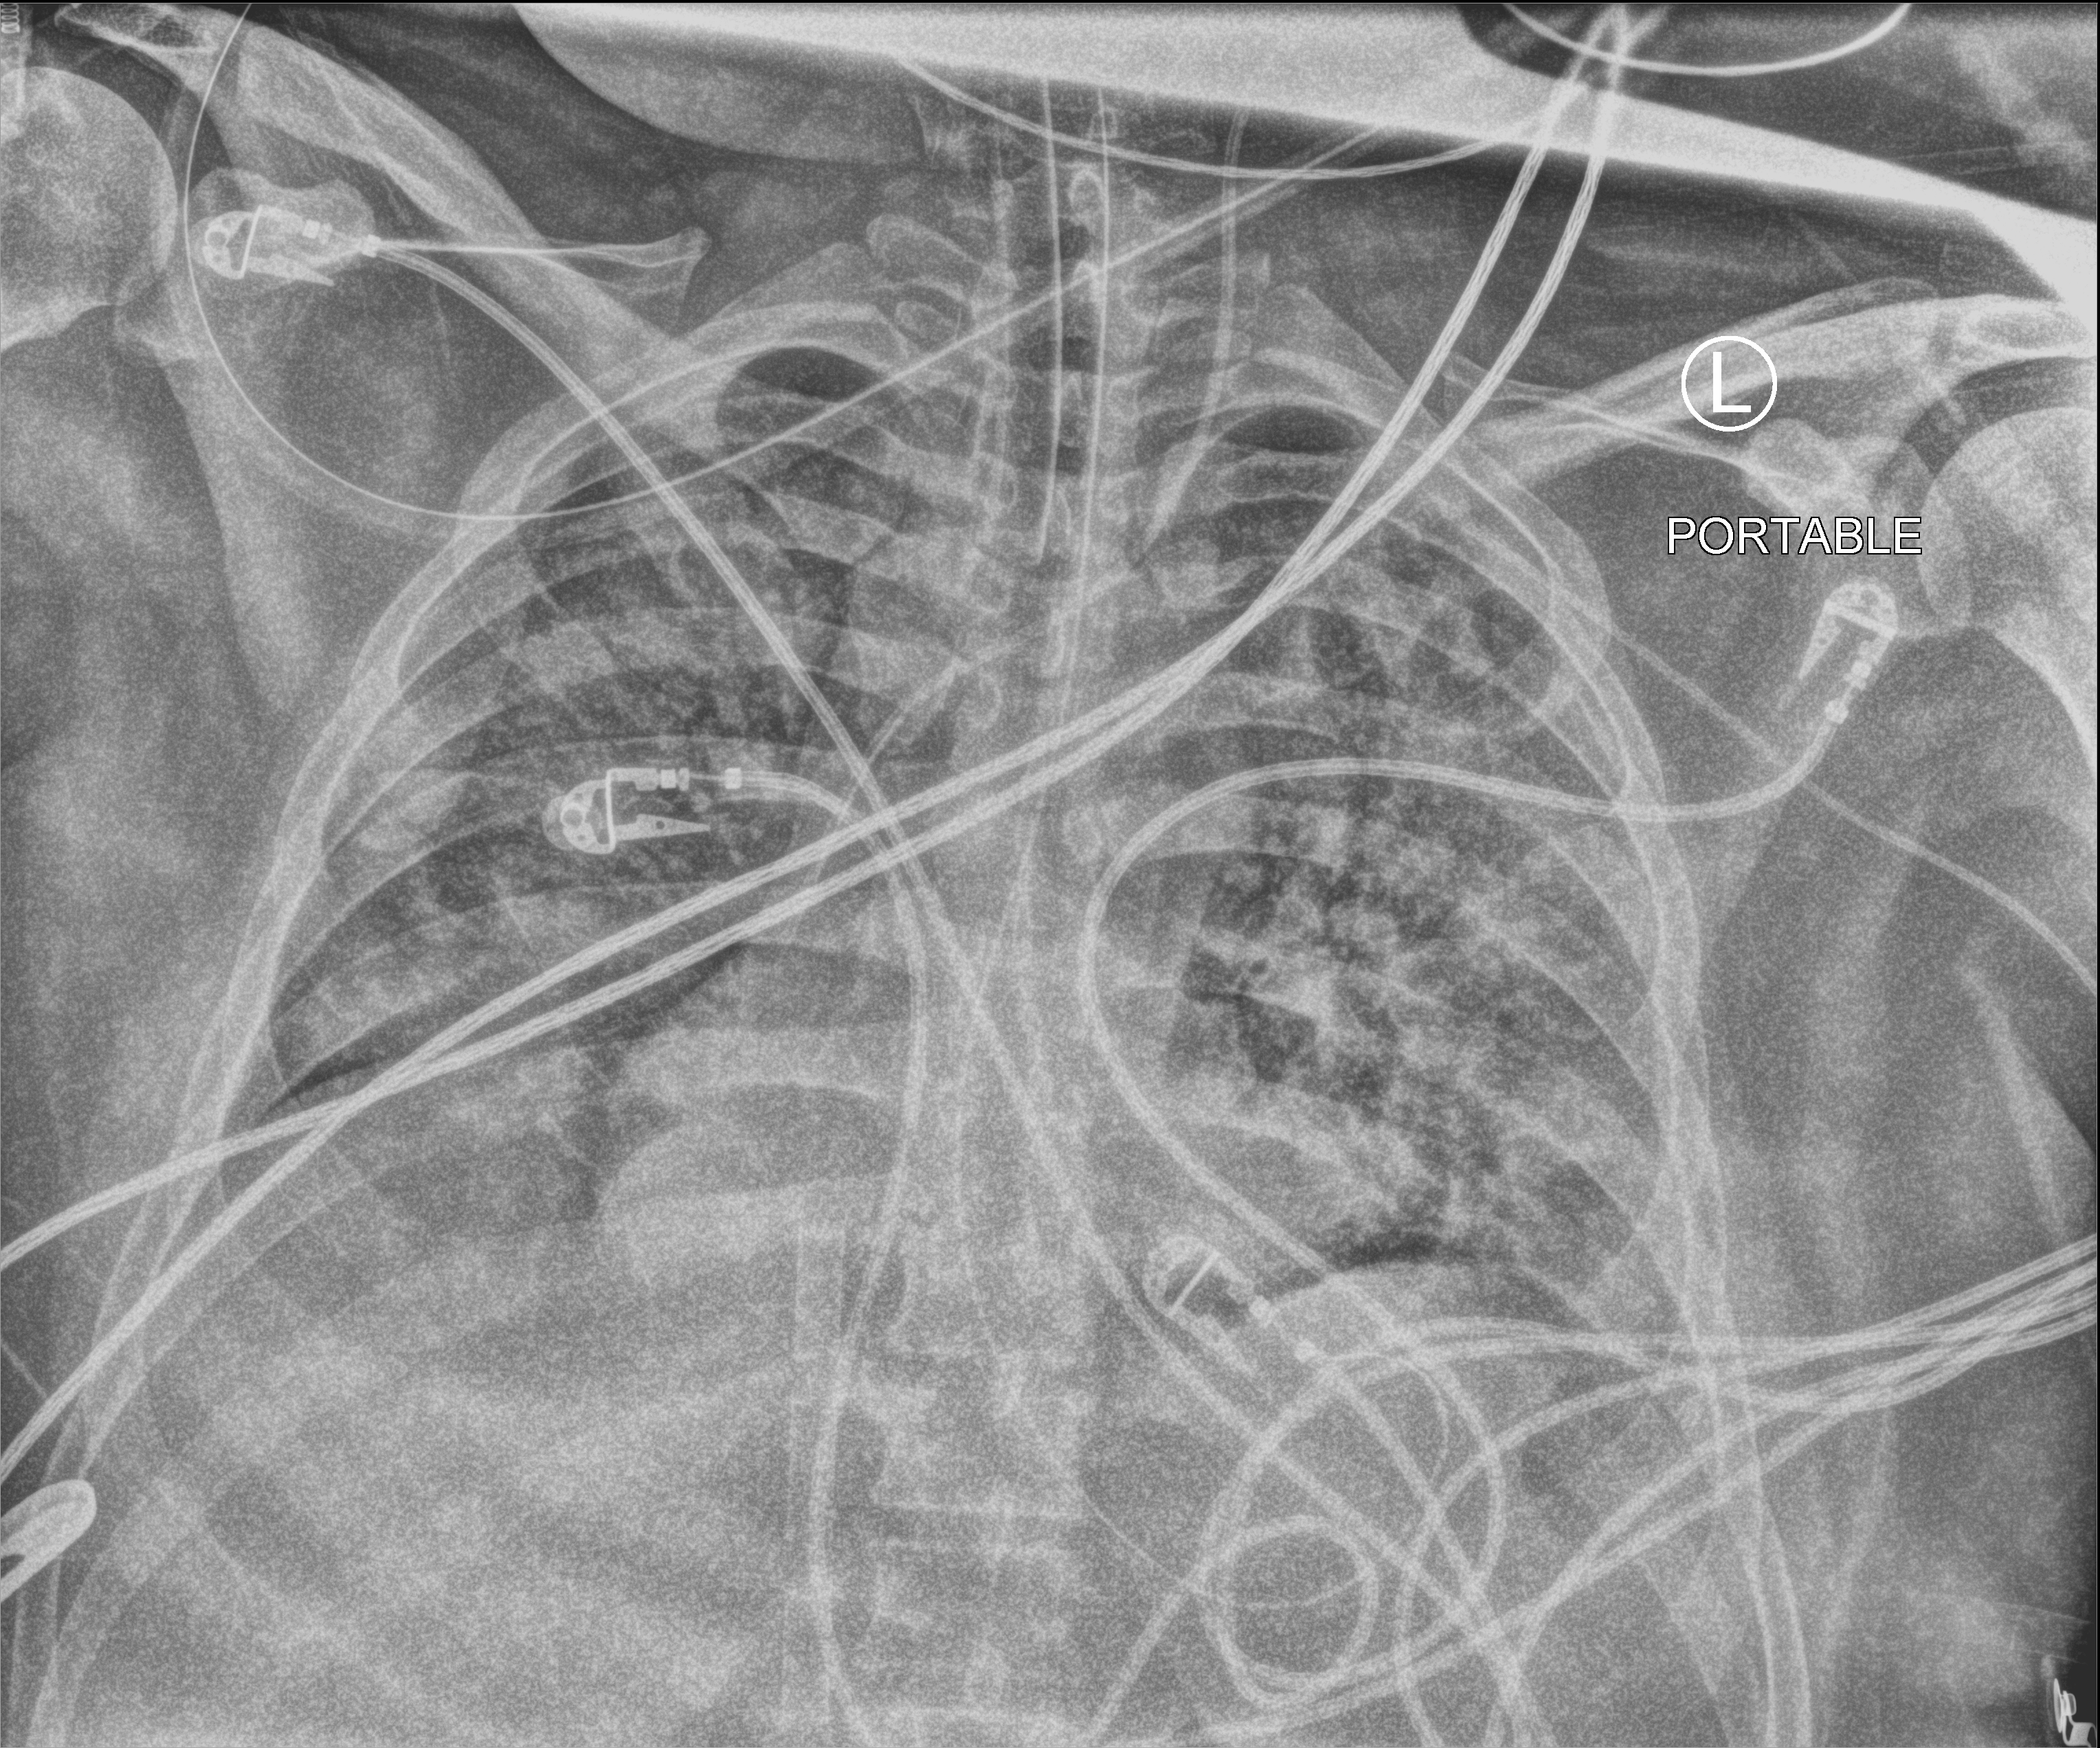
Portable chest radiograph. Adult patient hospitalised with COVID-19, age 18–59 years.
From the hospital-stay record, not from the radiograph (when in the stay this image was taken is not recorded): admitted to intensive care during this hospital stay: yes.